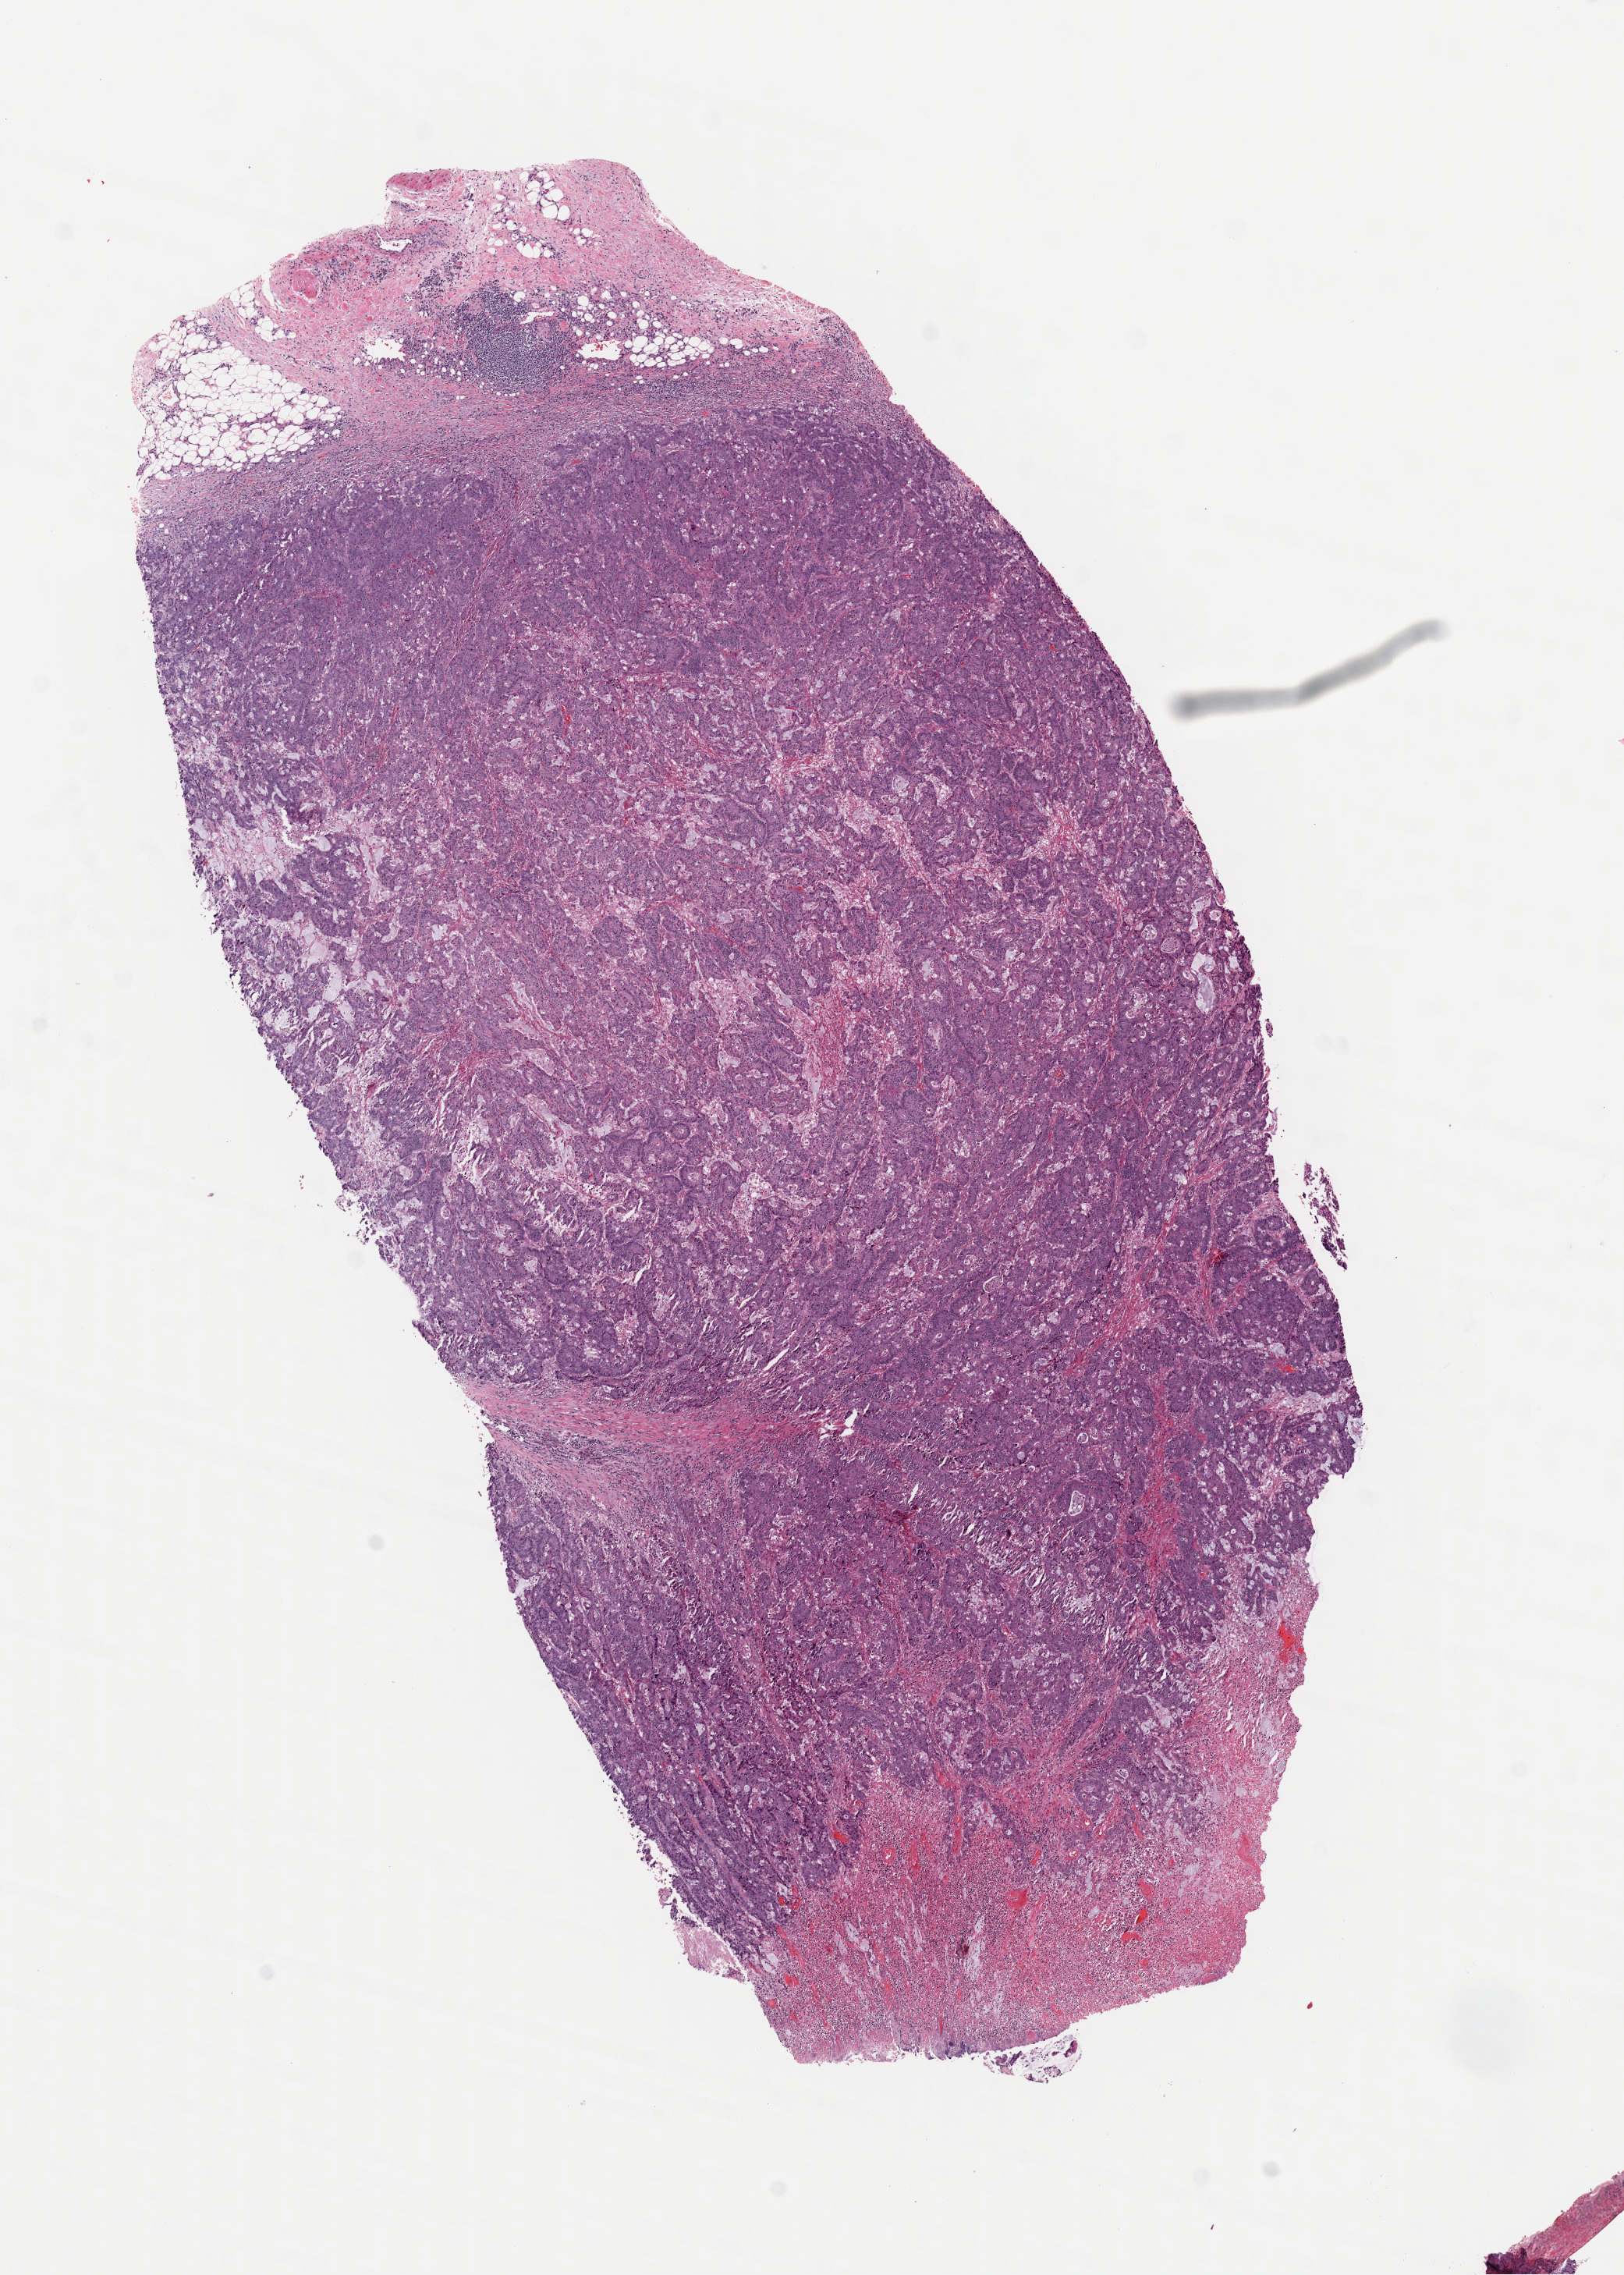
H&E-stained whole-slide image — shown as a low-resolution overview of the whole scanned area (about 8.2 x 11.5 mm, slide scanned at 40x), frozen section, colon, primary tumour sample. Patient: male, age at initial diagnosis 74 years. Slide review estimates, as recorded: tumour cells 90%, tumour nuclei 90%, normal cells 3%, stromal cells 7%, necrosis 0%. Infiltration values recorded for this section: lymphocyte infiltration 0%, monocyte infiltration 0%, neutrophil infiltration 0%.
AJCC pathologic stage: IIA (7th edition). Diagnosis: Mucinous adenocarcinoma (ascending colon).